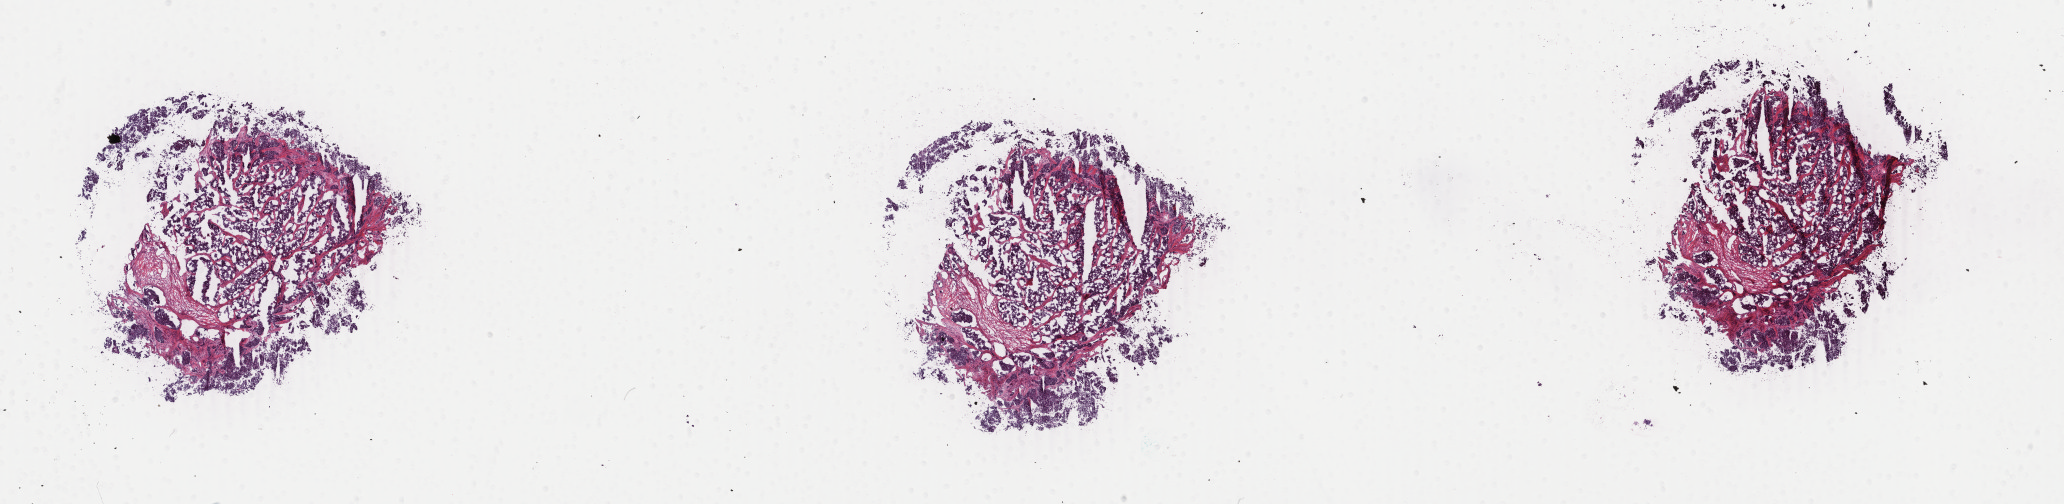
Digitized H&E-stained tissue section (whole slide), shown as a low-resolution overview of the whole scanned area (about 32.8 x 8.0 mm). Frozen section. Breast, primary tumour sample. Female patient; age at initial diagnosis 51 years. Composition of this section per pathologist review: tumour cells 85%, tumour nuclei 85%.
Histologic diagnosis: Infiltrating duct mixed with other types of carcinoma.